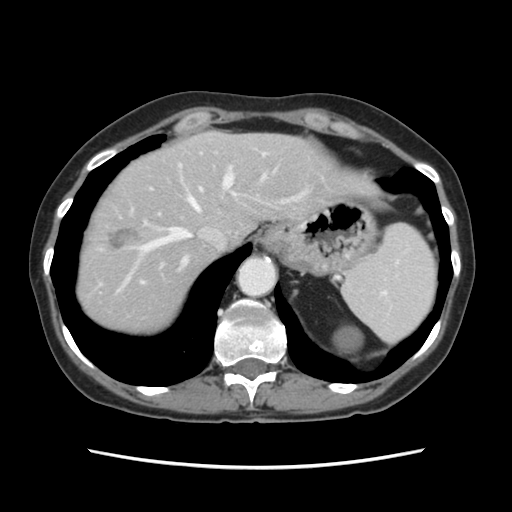
Contrast-enhanced abdominal CT, one axial slice. Position 97 of 120 along the scan axis. Soft-tissue window (W 400 / L 40 HU). 2.5 mm slice thickness. 512 × 512 image matrix, field of view 330 × 330 mm. Female patient, age 70 years. Case-level facts recorded for this patient, not image findings: diagnosis: colorectal cancer liver metastases, imaged before liver resection; multiple liver metastases: no; largest metastasis: 2.5 cm; chemotherapy before resection: yes.
Outlined on this slice (manually delineated by an expert):
- hepatic veins: bounding box <119,167,265,291> (left, top, right, bottom; pixels)
- liver: <78,132,362,333>
- planned liver remnant (the part of the liver to remain after resection): <141,132,360,270>
- portal vein (with intrahepatic branches): <141,153,266,283>
- liver metastasis: <110,229,138,250>